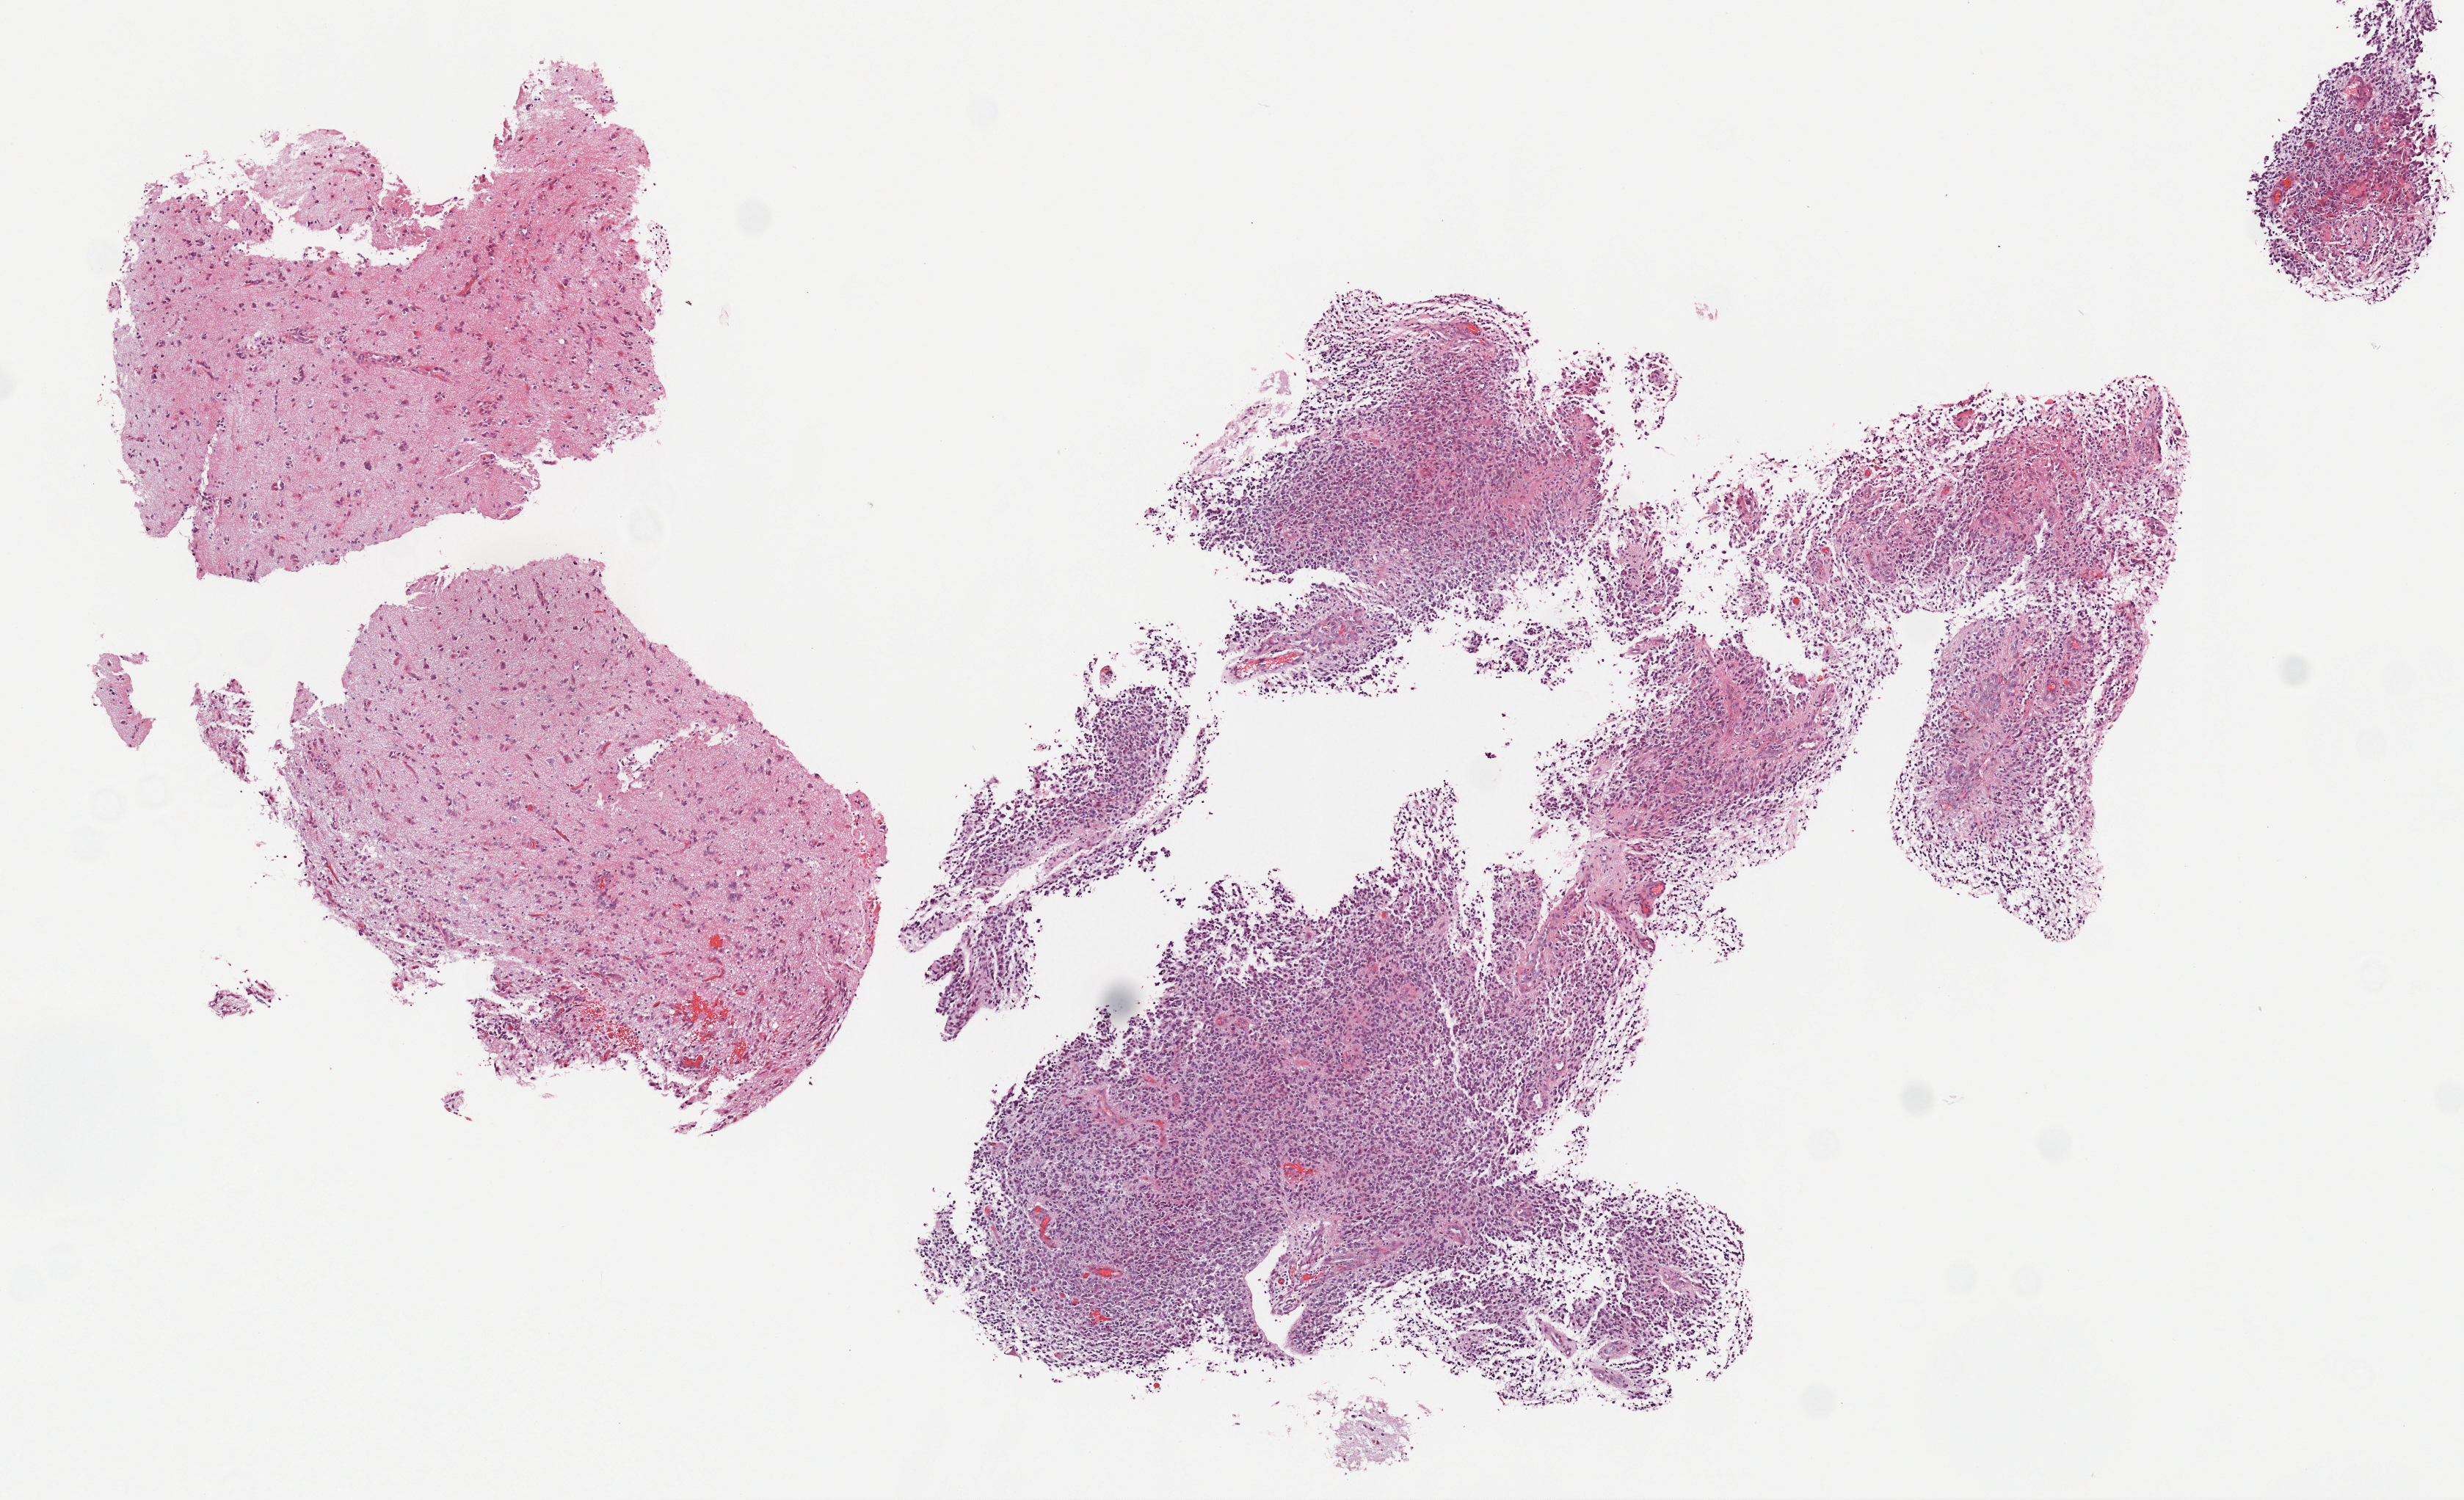
Whole-slide histology image, H&E — shown as a low-resolution overview of the whole scanned area (about 6.8 x 4.1 mm). FFPE section. Brain, primary tumour sample. Patient: female, age at initial diagnosis 60 years. Histologic grade: G3 (poorly differentiated).
Laterality: left. Pathologic diagnosis: Oligodendroglioma, NOS (cerebrum).